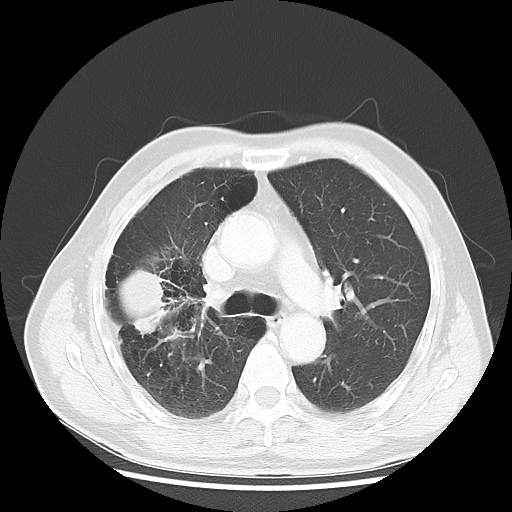
Chest CT, one axial slice. Reconstruction kernel LUNG. Lung window (W 1500 / L -600 HU). 5 mm slice thickness. 512 × 512 image matrix. Patient: male, 69 years. From the clinical record (not read from this slice): clinical TNM (as recorded): T3 N0 M0; histopathological grade: G3.
Outlined on this slice (bounding box drawn by a radiologist):
- lung tumour (recorded histology: adenocarcinoma): bounding box [x1, y1, x2, y2] px = [109, 262, 168, 339]